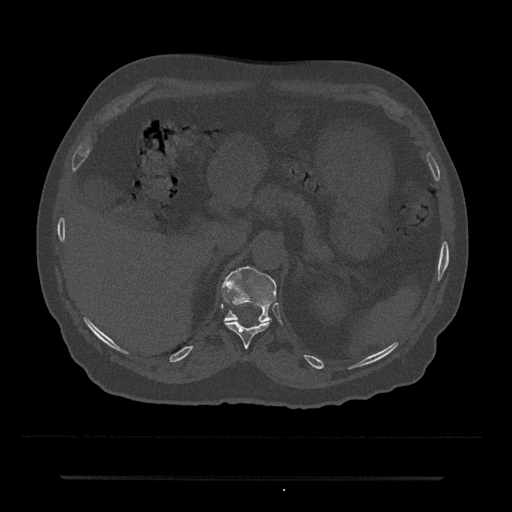
CT including the spine, one axial slice. Slice 160 of 797 in the series (ordered by position). Reconstruction kernel Br40s/3. 120 kVp. Bone window (W 1800 / L 400 HU). 0.5 mm slice thickness. 512 × 512 image matrix, field of view 437 × 437 mm. Male patient, age 69 years. Case-level facts recorded for this patient, not image findings: primary cancer: prostate.
Outlined on this slice (semi-automatic segmentation, software-assisted and operator-edited):
- T11 vertebra: bounding box (x1, y1, x2, y2) in pixels: (225, 322, 269, 348)
- T12 vertebra: (223, 266, 277, 322)